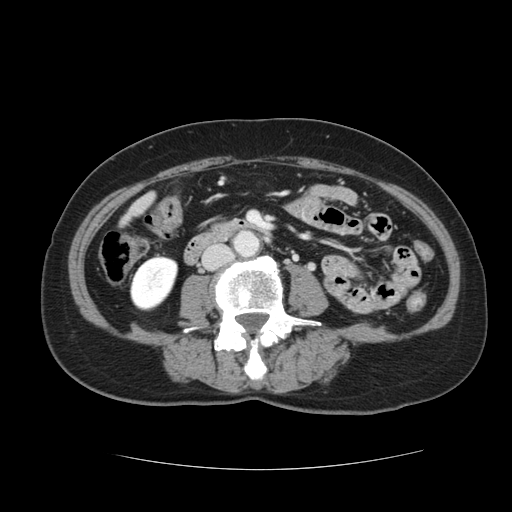
Contrast-enhanced abdominal CT, one axial slice; slice 12 of 128 in the series (ordered by position); 120 kVp; intravenous contrast given; soft-tissue window (W 400 / L 40 HU); 2.5 mm slice thickness; 512 × 512 image matrix, field of view 366 × 366 mm. Female patient, age 67 years. Case-level facts recorded for this patient, not image findings: diagnosis: colorectal cancer liver metastases, imaged before liver resection; multiple liver metastases: yes; largest metastasis: 3 cm; chemotherapy before resection: no.
Outlined on this slice (outlined manually by an expert reader):
- liver: bounding box <133,197,150,213> (left, top, right, bottom; pixels)
- planned liver remnant (the part of the liver to remain after resection): <132,209,138,214>